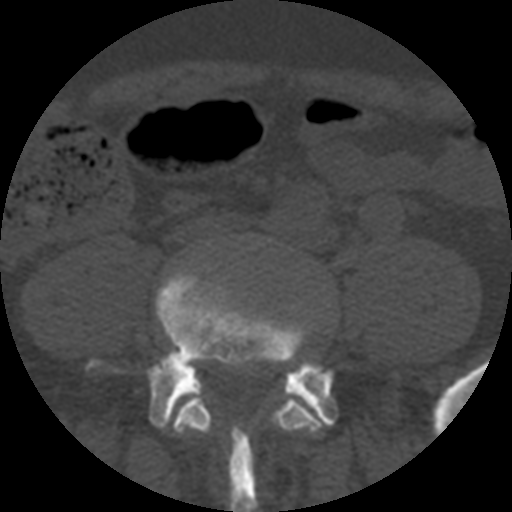
CT including the spine, one axial slice. Slice 74 of 508 in the series (ordered by position). Reconstruction kernel STANDARD. Bone window (W 1800 / L 400 HU). 512 × 512 image matrix, field of view 160 × 160 mm. Patient age 57 years. From the clinical record (not read from this slice): primary cancer: prostate.
Structures marked on this image (semi-automatically segmented with operator editing):
- L4 vertebra: bounding box <173,389,325,436> (left, top, right, bottom; pixels)
- L5 vertebra: <89,270,336,512>